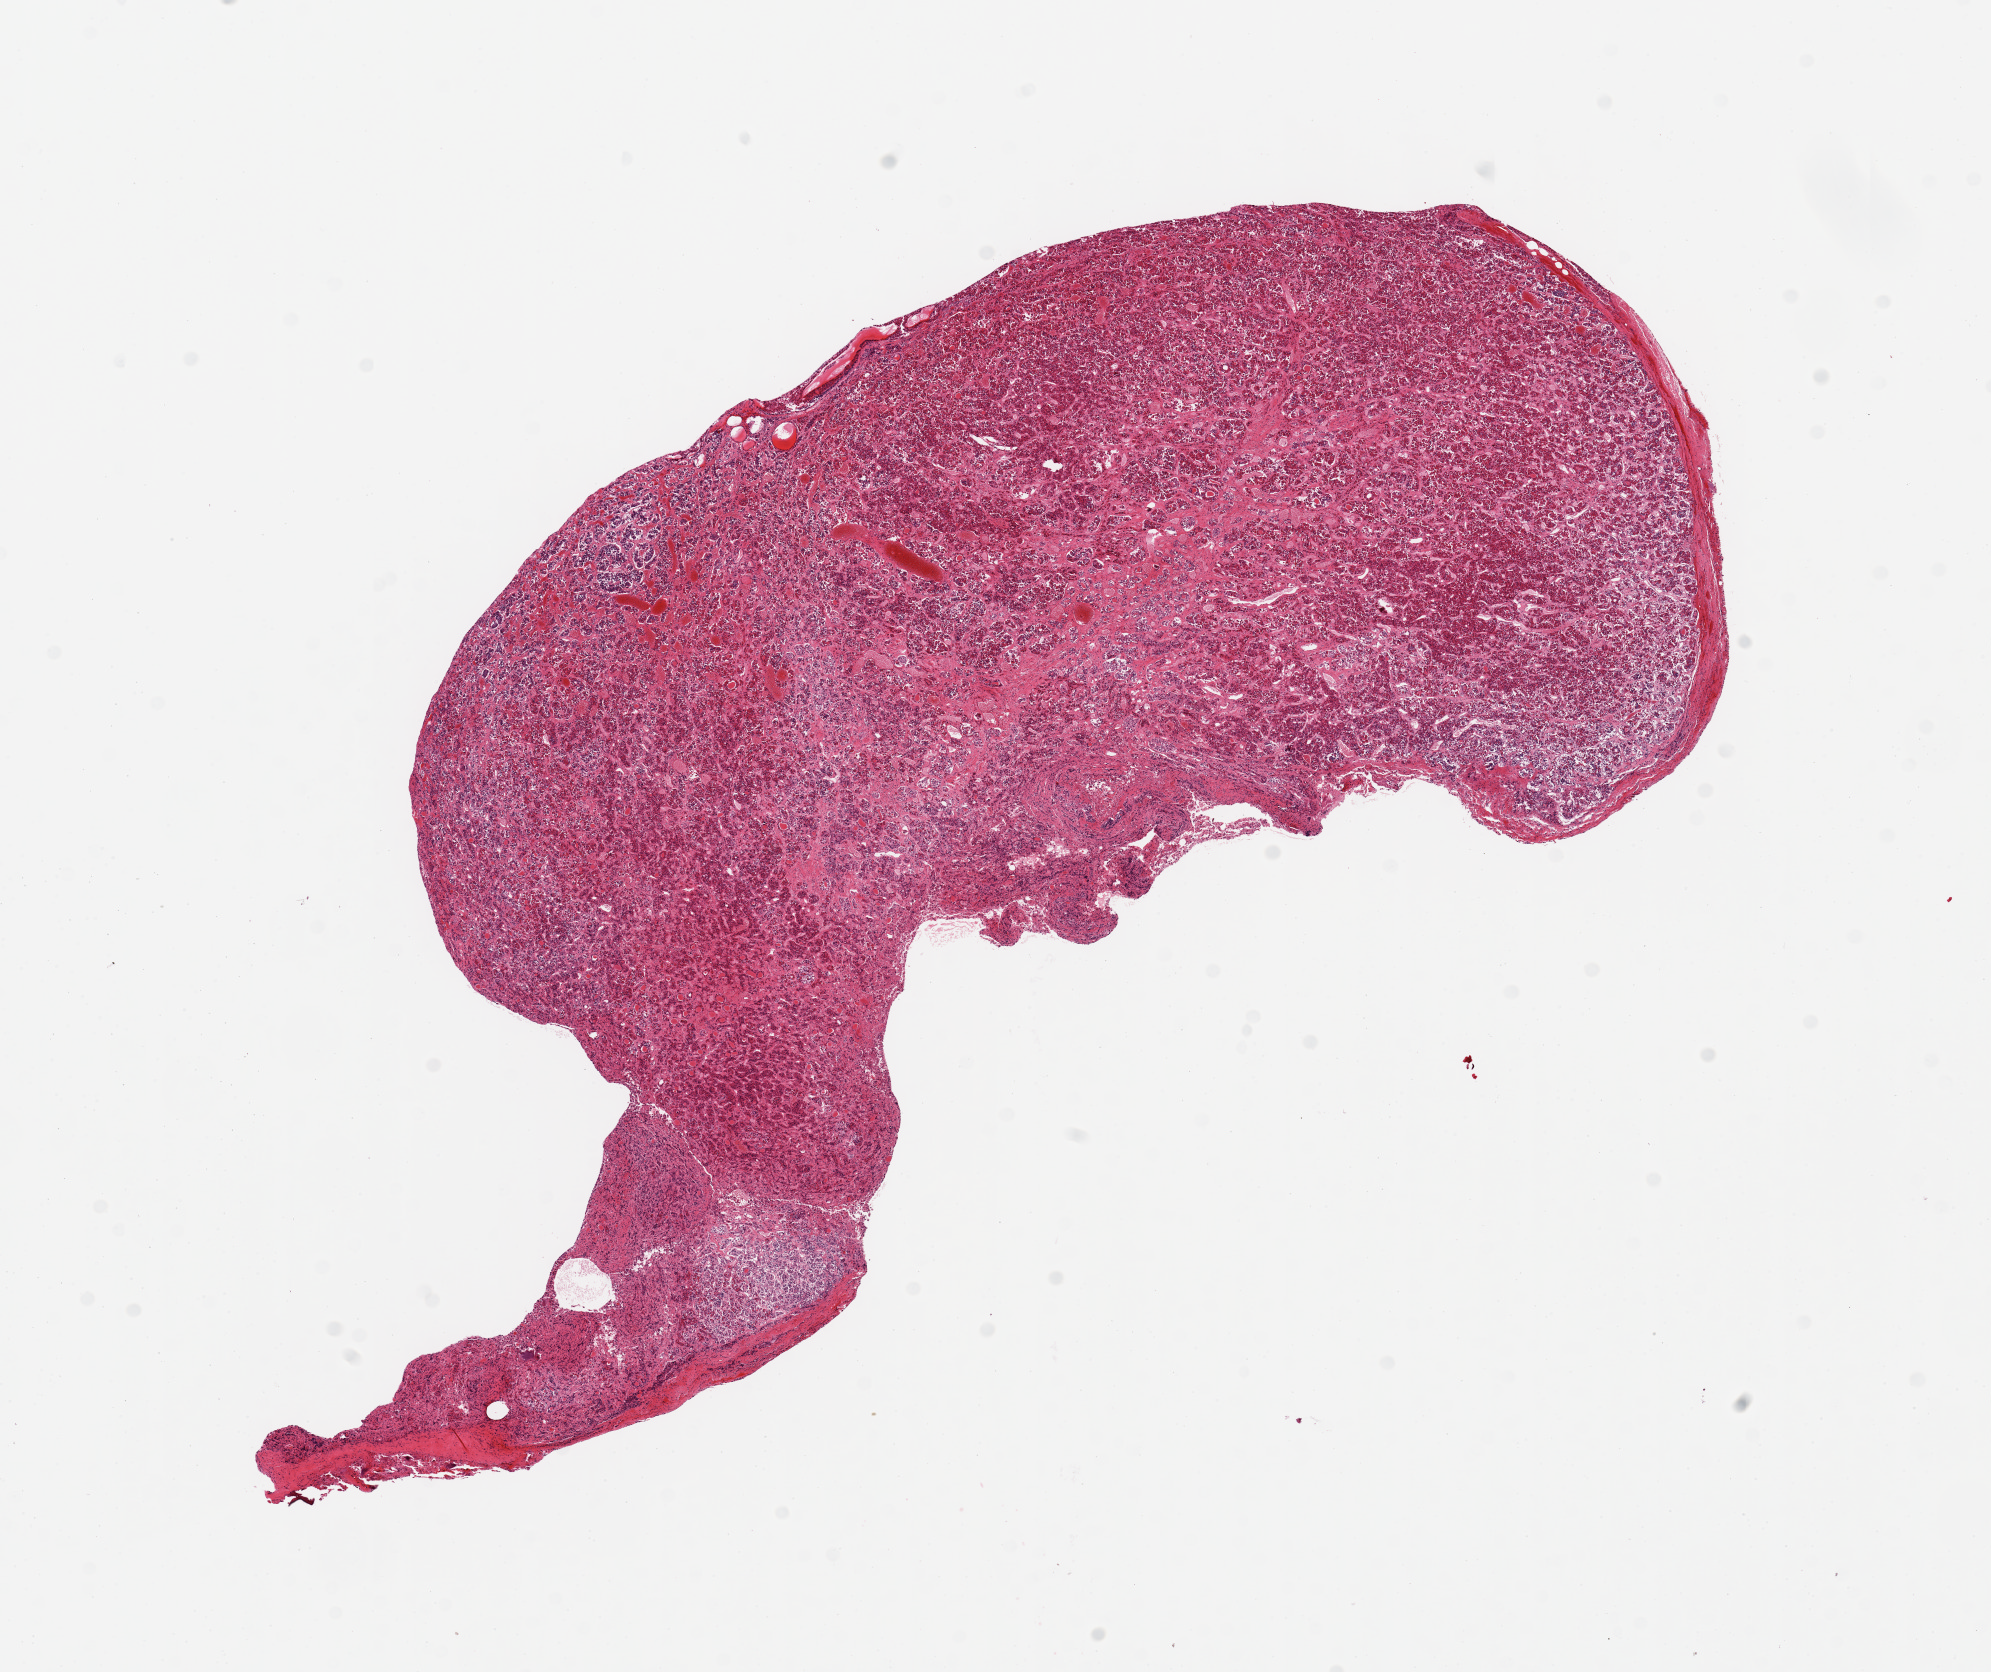
Whole-slide image, H&E stain — whole scanned area (about 15.8 x 13.2 mm) shown as a low-resolution overview. PAXgene-fixed paraffin-embedded (PFPE) section. Section of pituitary (target tissue). Donor tissue sample. Male donor.
Reviewer comment on this tissue sample: 1 piece.